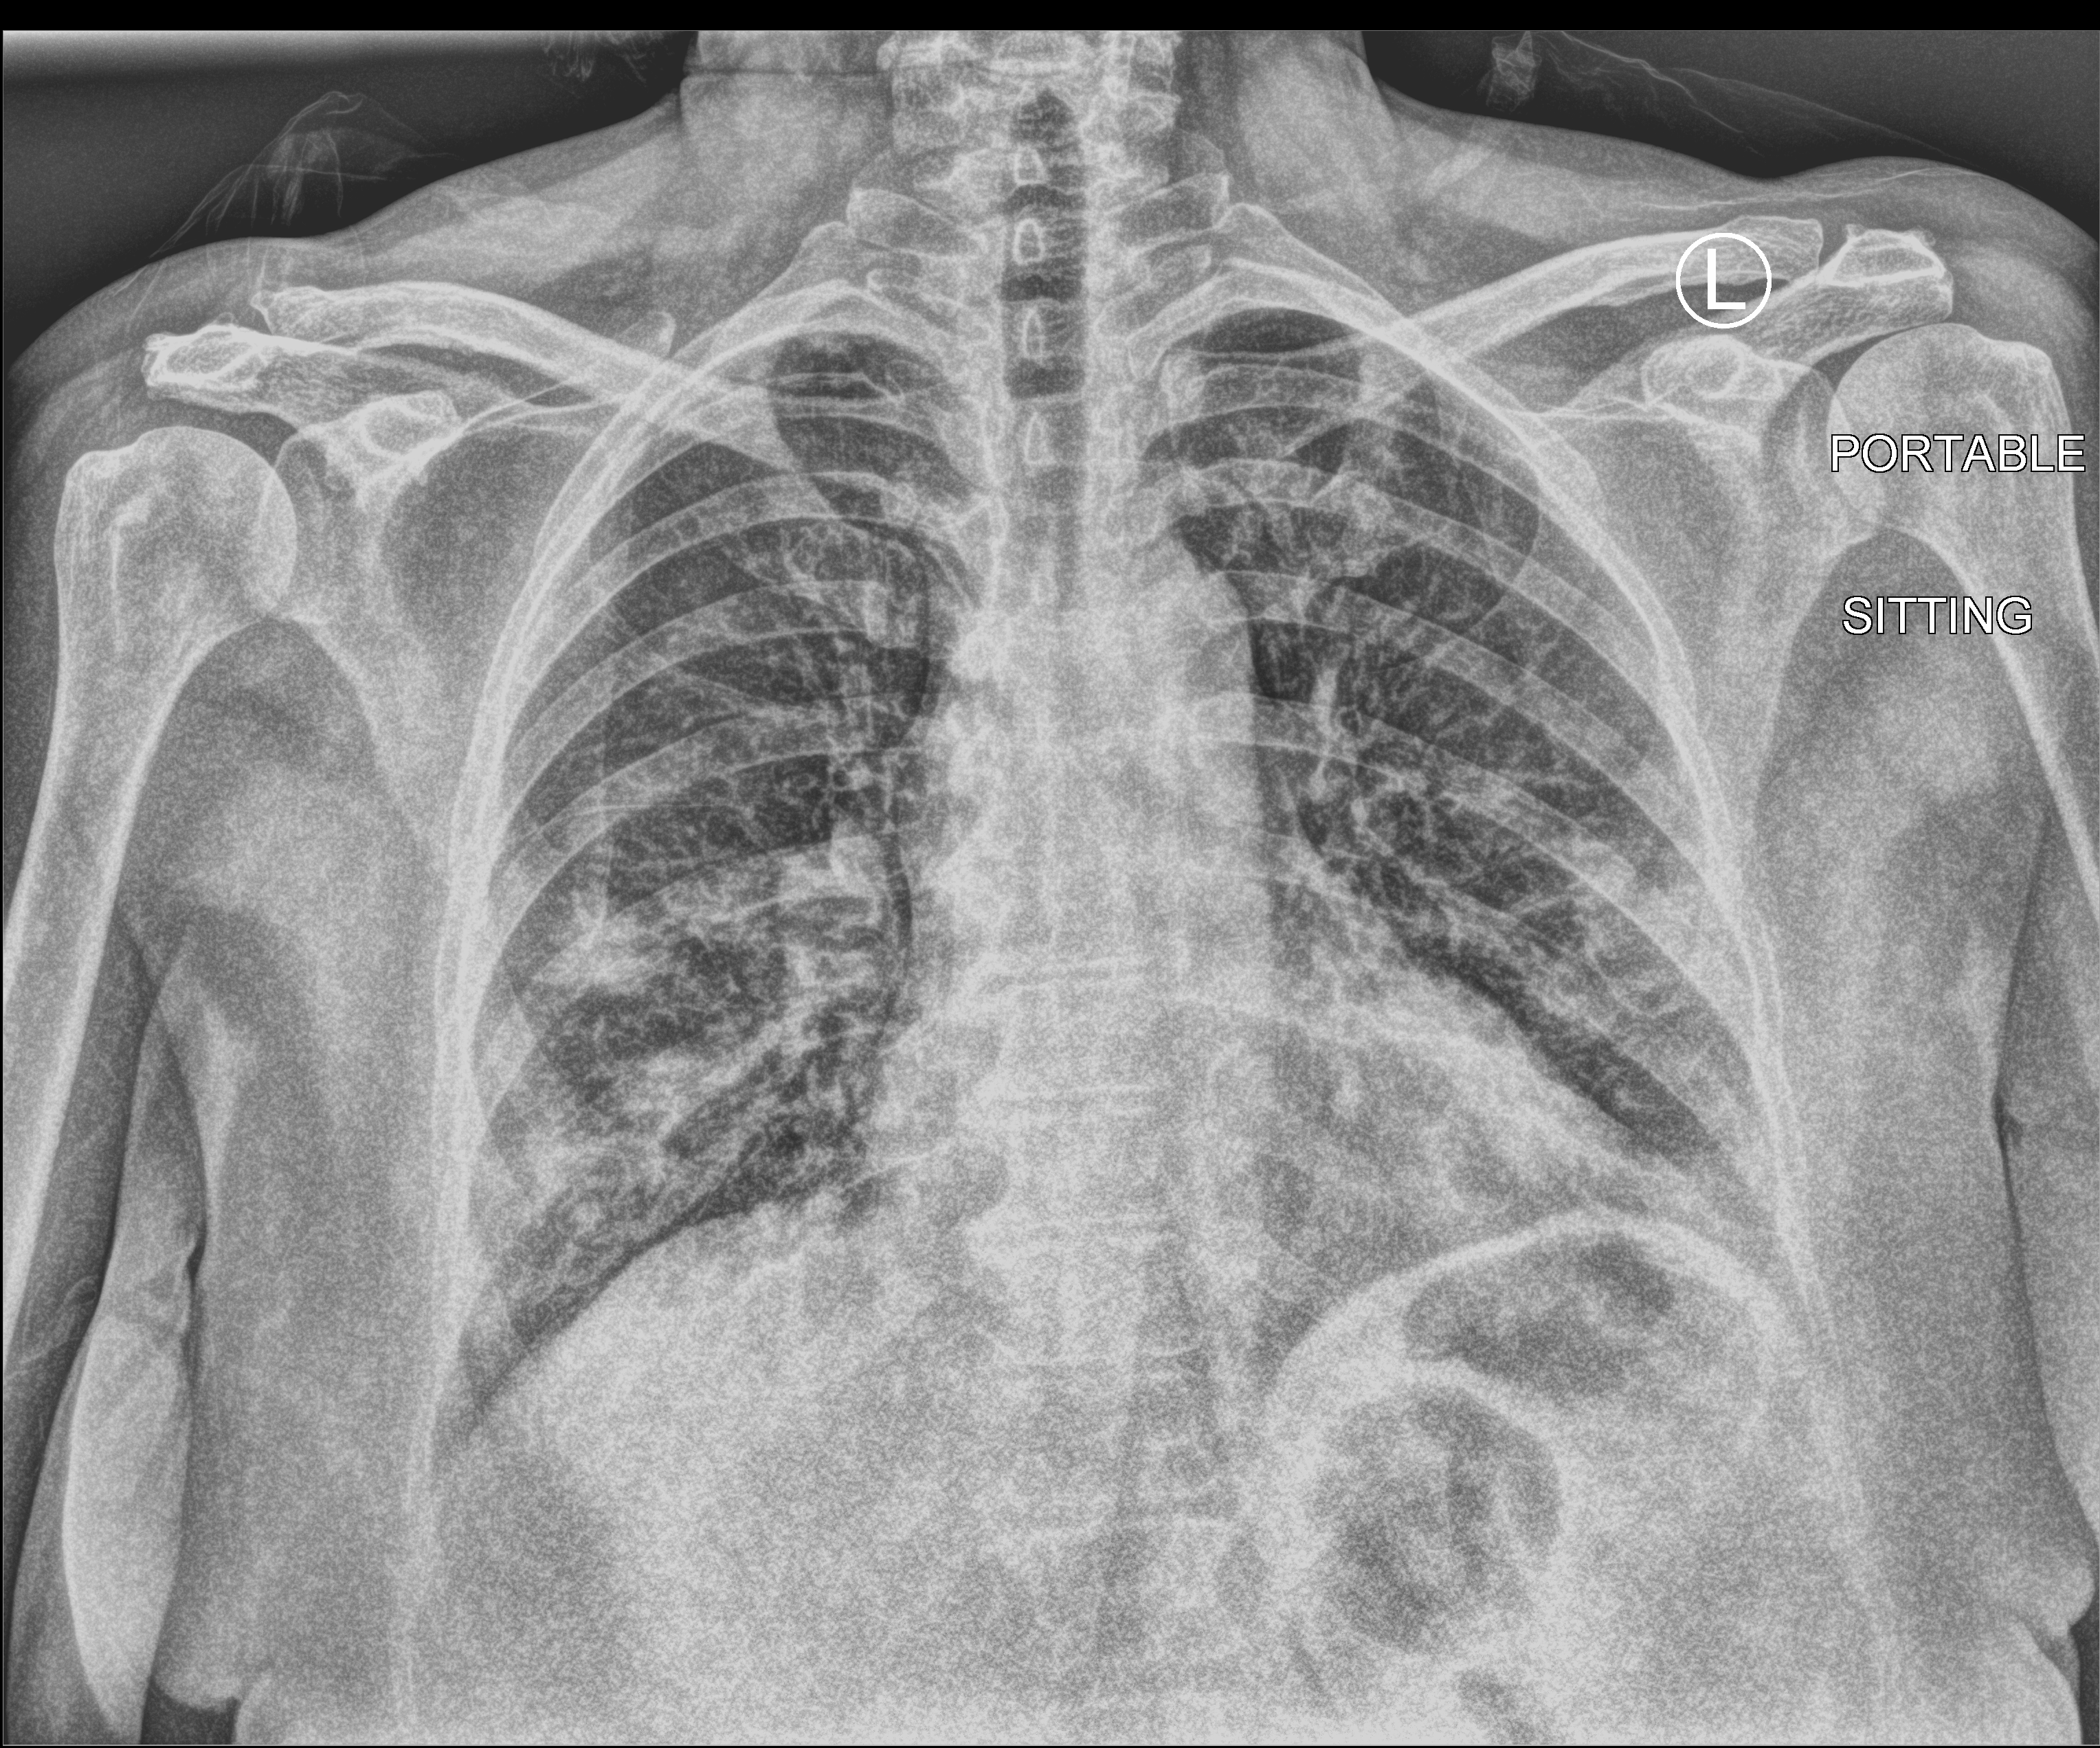
Portable chest radiograph. Female patient hospitalised with COVID-19, age 60–74 years.
Hospital-stay facts (about this admission, not read from this image; timing relative to this image not recorded):
- diabetes (admission record): no